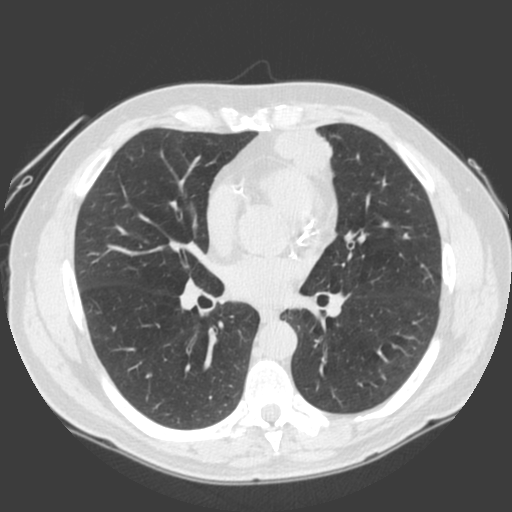
Low-dose screening chest CT, one axial slice; position 93 of 185 along the scan axis; lung window (W 1500 / L -600 HU); 2 mm slice thickness; 512 × 512 image matrix.
Annotated regions visible in this slice (expert manual segmentation):
- lesion 1 (tumor, lower lobe of left lung): box from (x=275, y=126) to (x=333, y=173) px